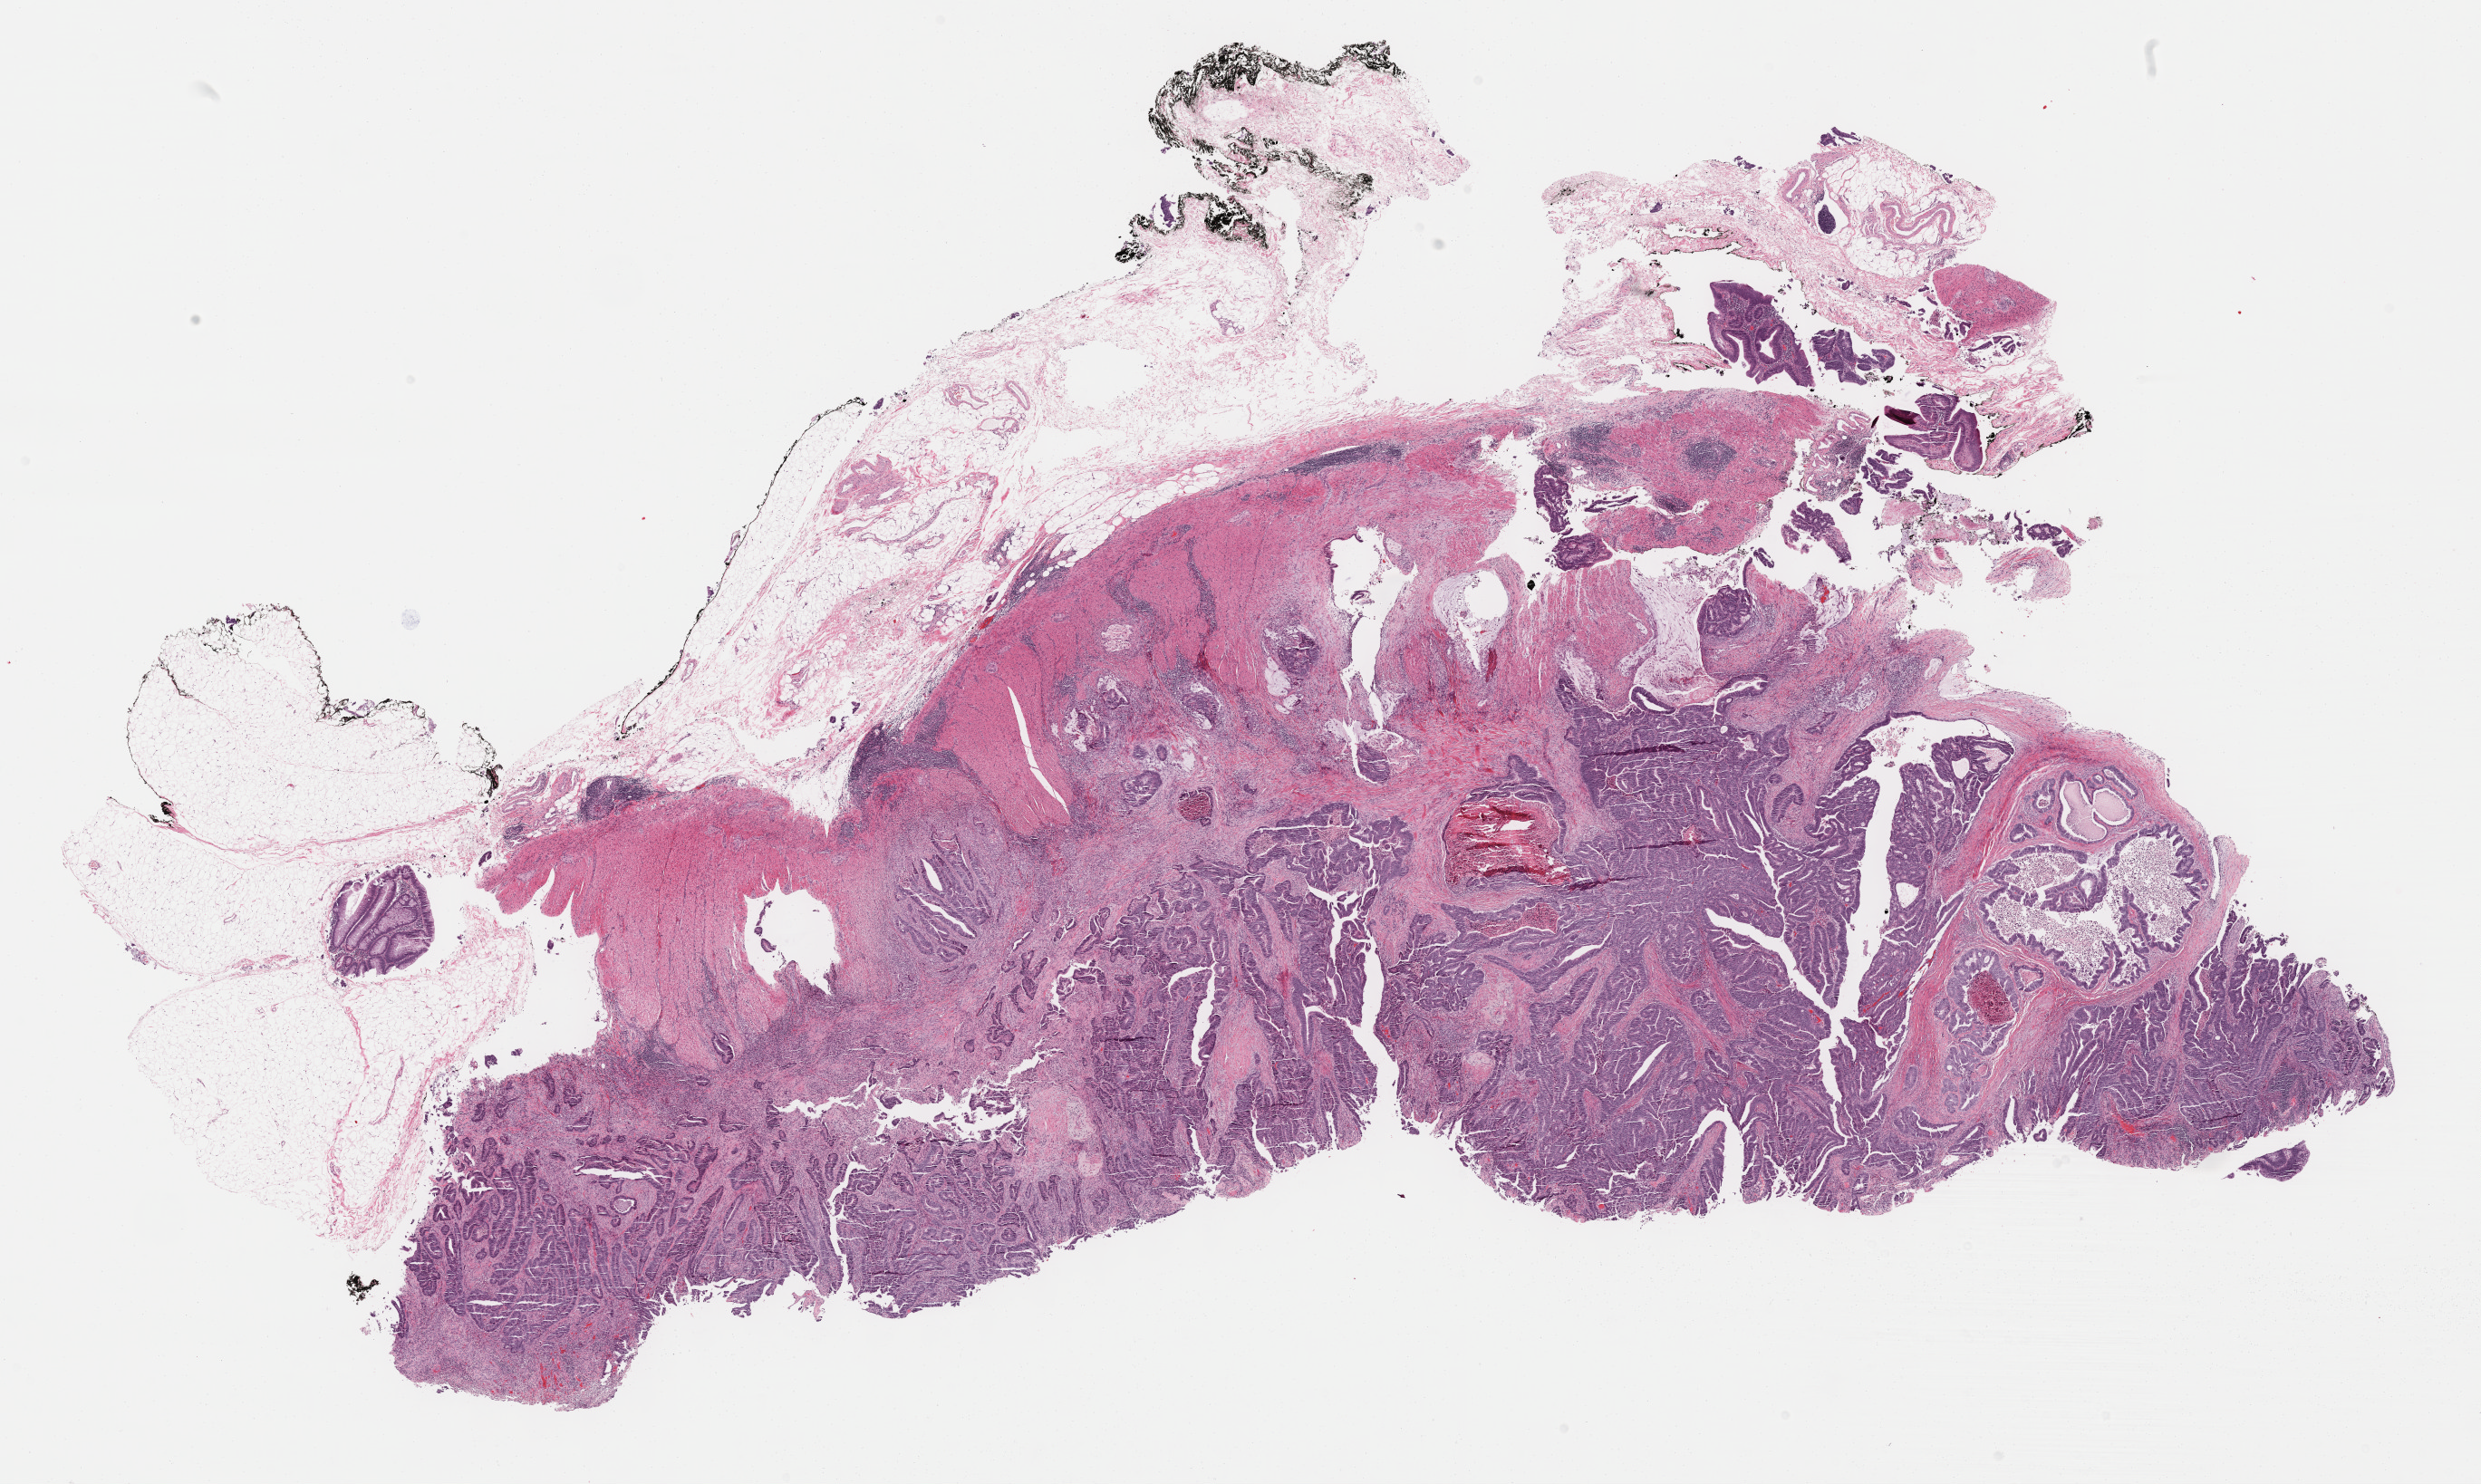
H&E whole-slide image, whole scanned area (about 22.1 x 13.3 mm, slide scanned at 40x) shown as a low-resolution overview, formalin-fixed paraffin-embedded (FFPE) diagnostic section, primary tumour sample from the colon. Female patient; age at initial diagnosis 61 years.
Lymph nodes positive (case pathology): 0 of 28 examined. Diagnosis: Adenocarcinoma, NOS. AJCC pathologic stage: I (7th edition).